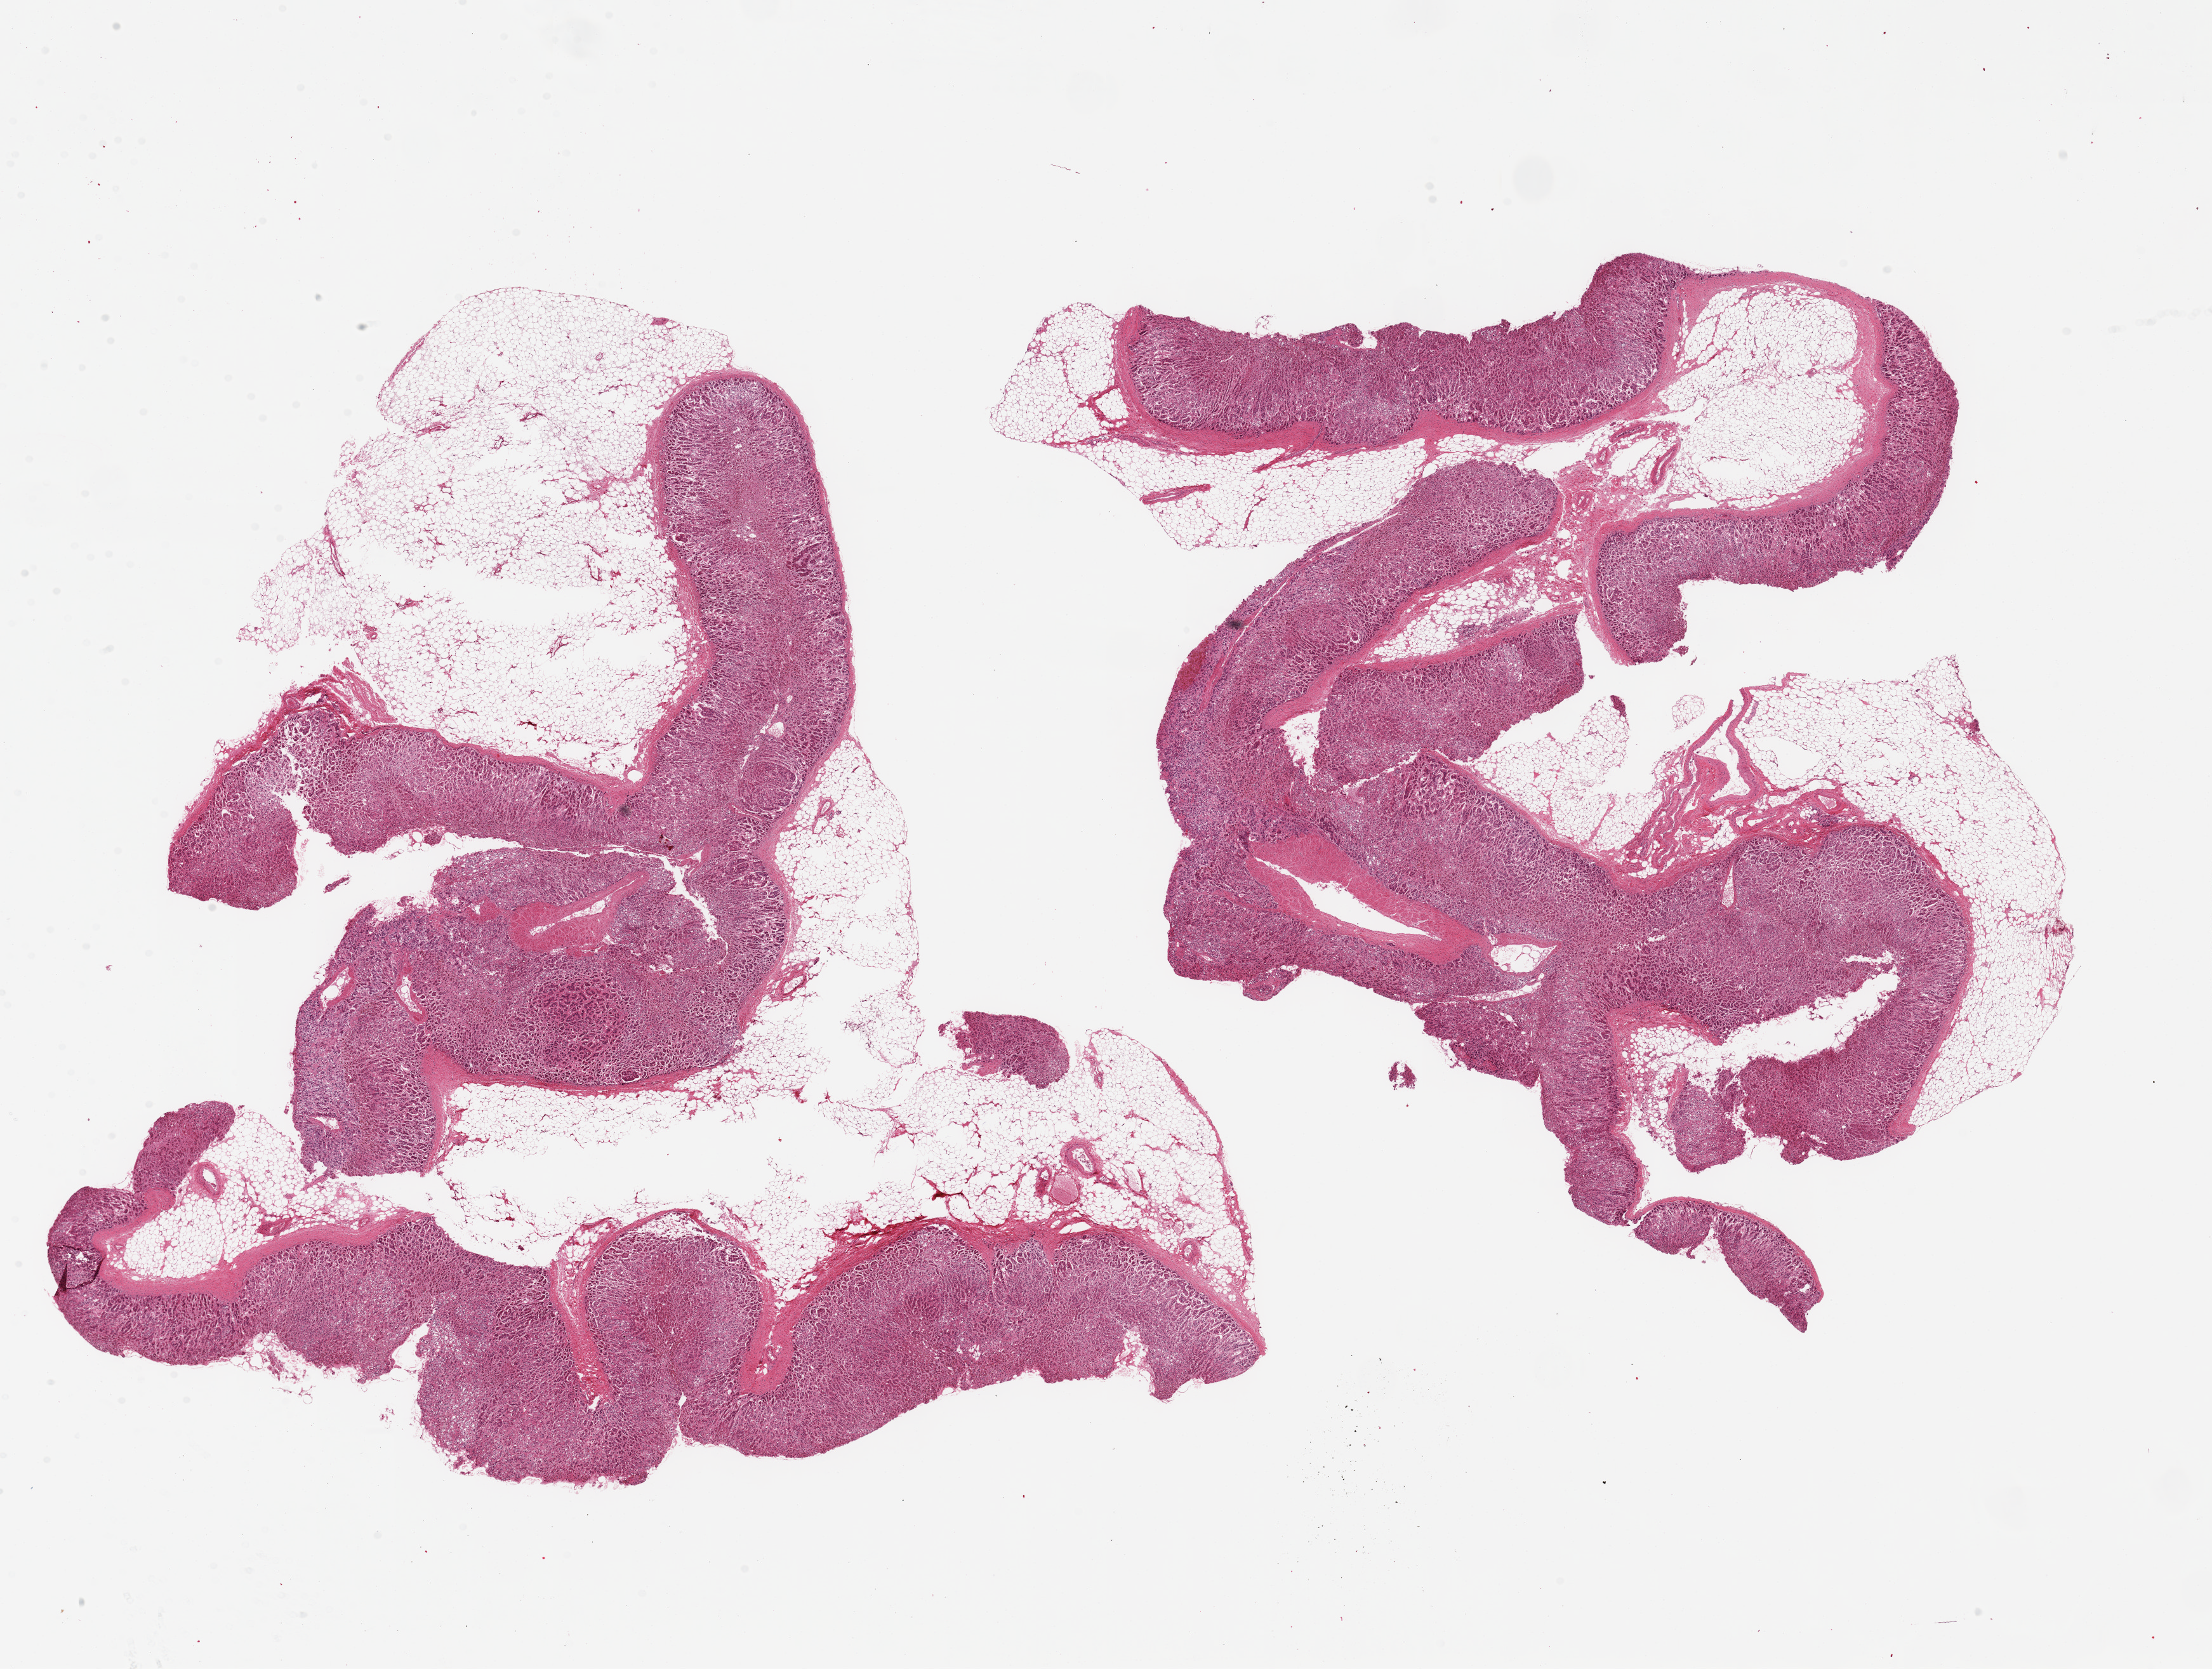
Whole-slide image, H&E stain, shown as a low-resolution overview of the whole scanned area (about 27.6 x 20.8 mm, acquisition: 20x scan); PAXgene-fixed, paraffin-embedded tissue; section of adrenal gland (target tissue); donor tissue sample. Donor sex: male.
Reviewer comment on this tissue sample: 2 ~12x10mm aliquots. ~40% peripheral fat.